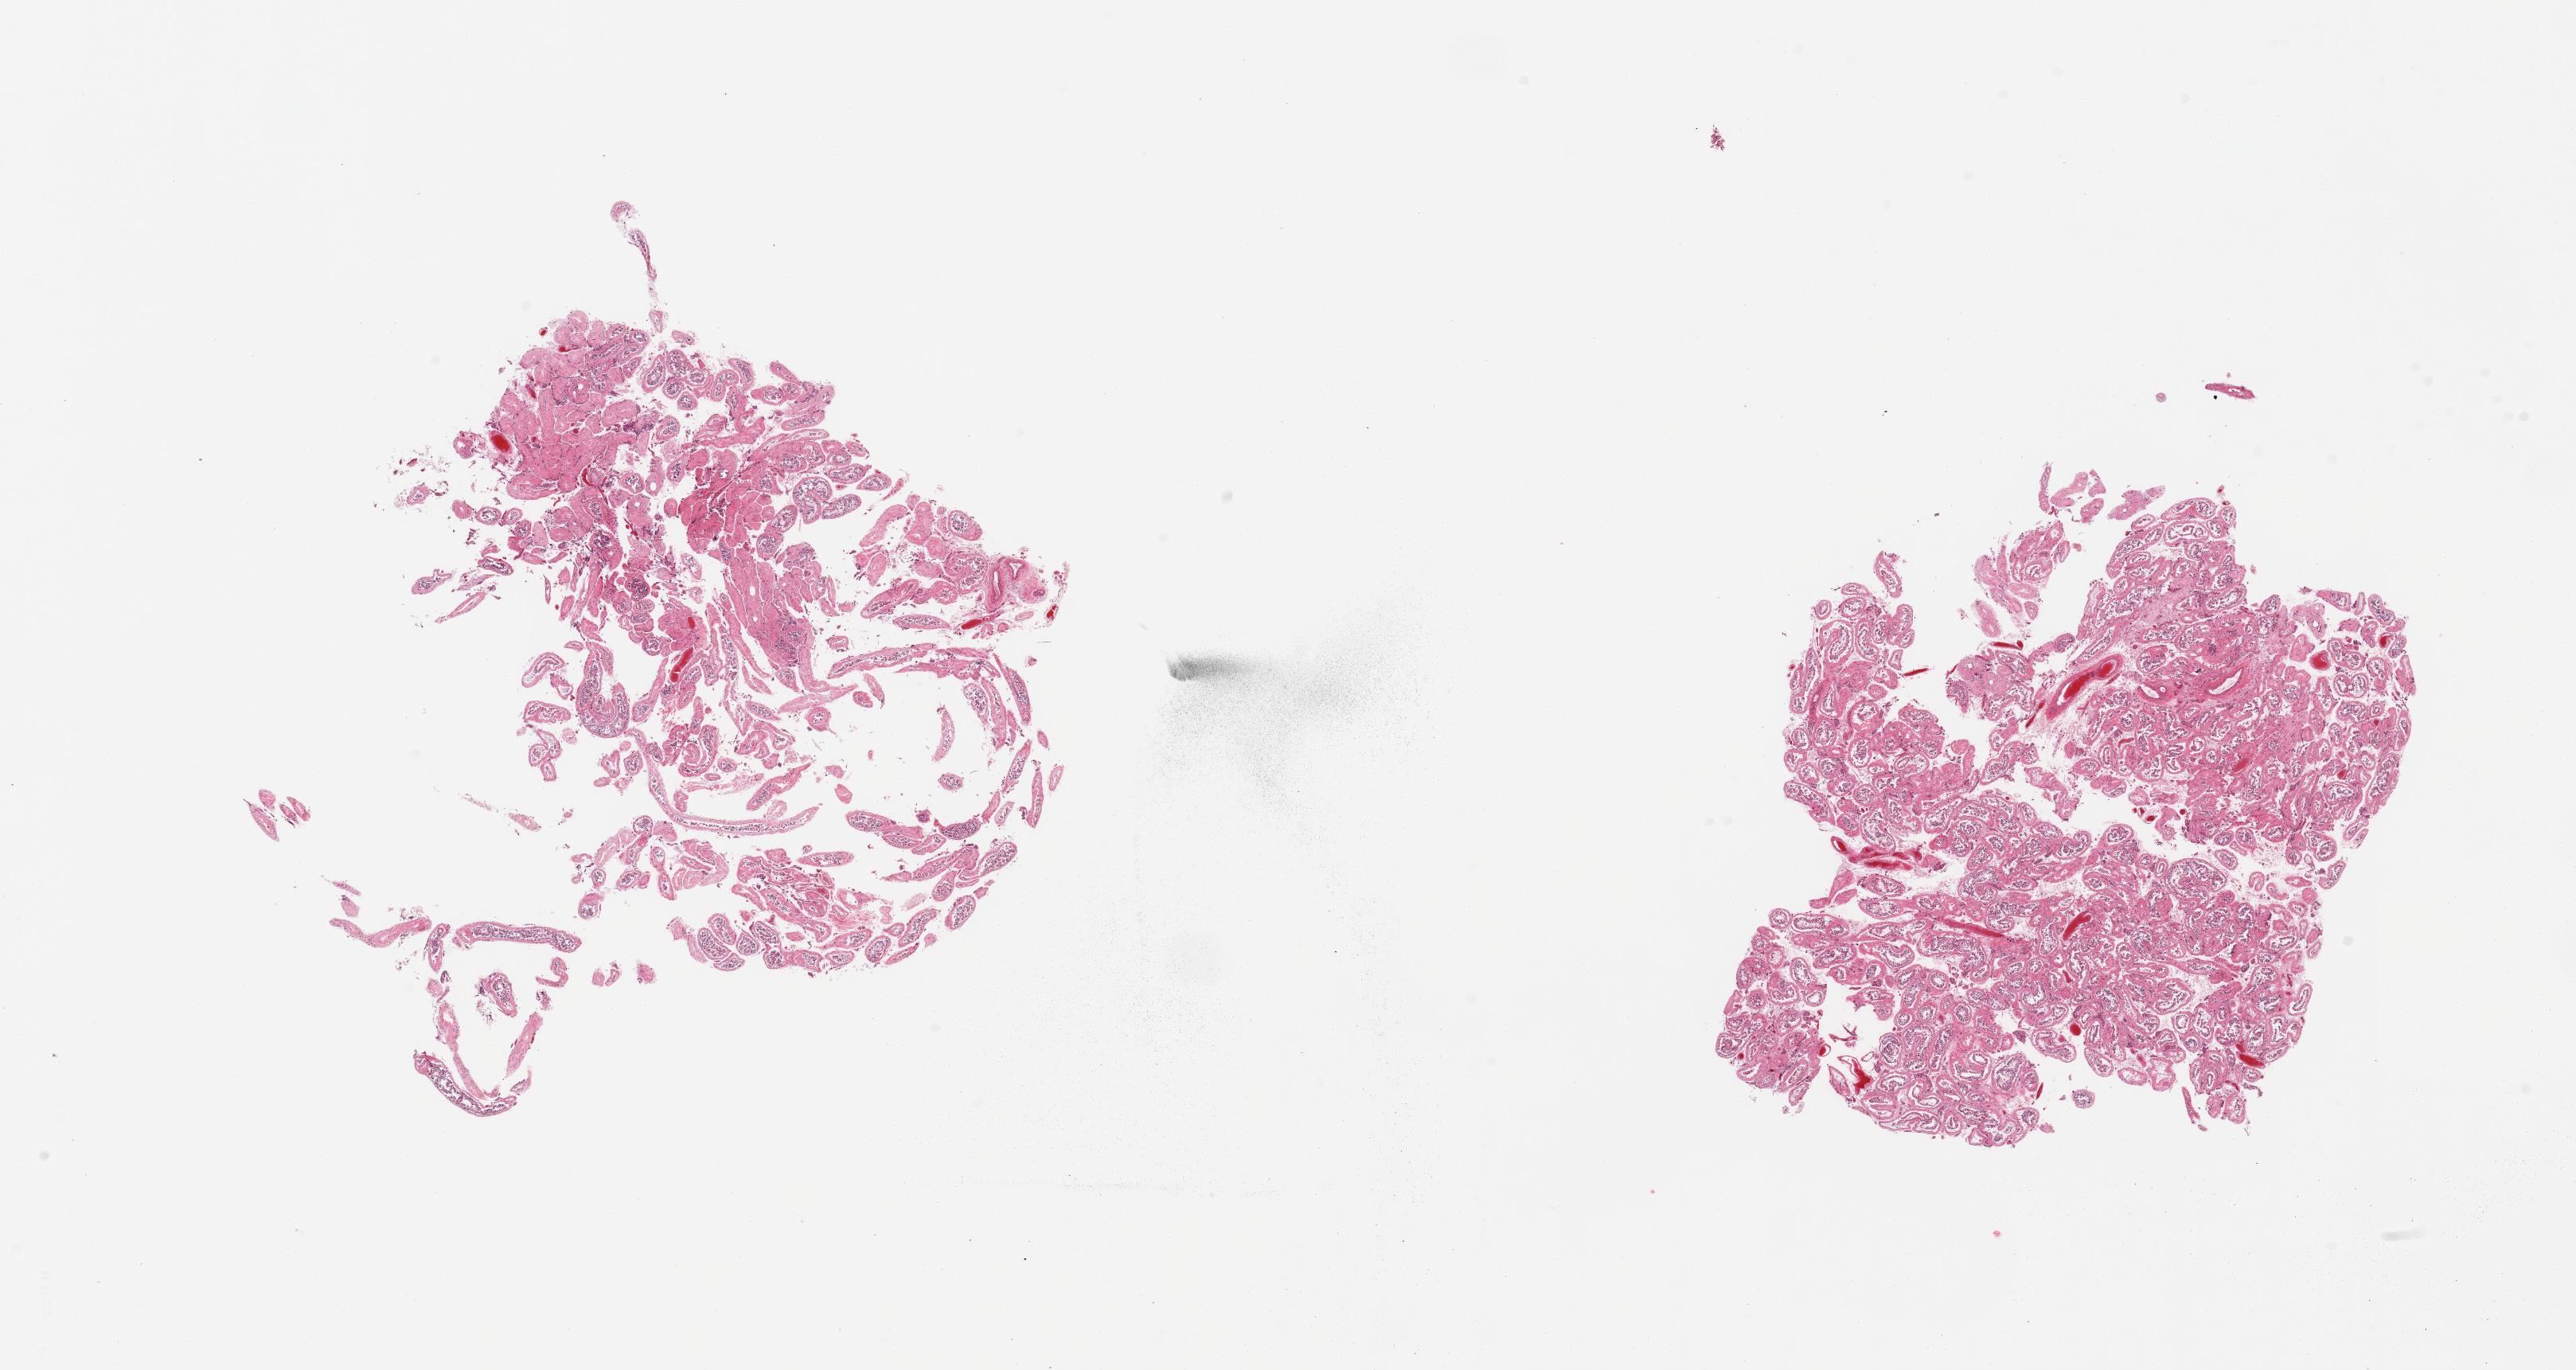
Digitized H&E-stained section — whole scanned area (about 25.6 x 13.6 mm, slide scanned at 20x) shown as a low-resolution overview; PAXgene-fixed paraffin-embedded (PFPE) section; target tissue: testis; tissue donor sample.
Reviewer comment on this tissue sample: 2 fragmented pieces; atrophic, greatly reduced spermatogenesis.